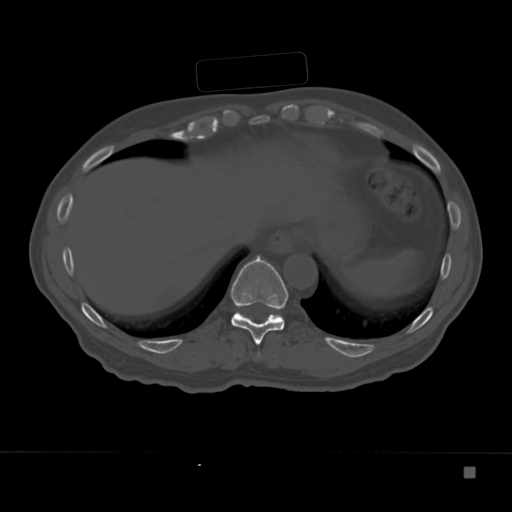
CT including the spine, one axial slice. Slice 170 of 332 in the series (ordered by position). Reconstruction kernel Br40s. 120 kVp. Bone window (W 1800 / L 400 HU). 1.5 mm slice thickness. 512 × 512 image matrix, field of view 389 × 389 mm. Patient: male, 72 years. From the clinical record (not read from this slice): primary cancer: skeletal.
Outlined on this slice (semi-automatically segmented with operator editing):
- T10 vertebra: bounding box <231,256,288,345> (left, top, right, bottom; pixels)
- T11 vertebra: <235,311,282,318>
- T9 vertebra: <258,353,261,356>